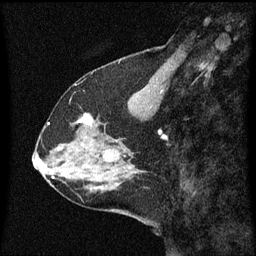
Breast MRI (dynamic contrast-enhanced), one sagittal slice; dynamic contrast-enhanced series, image 2 of 3 at this slice position (ordered by acquisition); 1.5 T; TE 4.2 ms, TR 8.4 ms; 256 × 256 image matrix, field of view 200 × 200 mm. Patient: female, 59 years.
Annotated regions visible in this slice (semi-automatic segmentation, software-assisted and operator-edited):
- analysis volume of interest (the breast-tissue region the enhancement analysis was run in; not a lesion): box from (x=73, y=114) to (x=99, y=137) px
- tumour enhancement mask (voxels above the 70 % enhancement threshold inside the analysis volume of interest): (x=79, y=114)–(x=94, y=125)